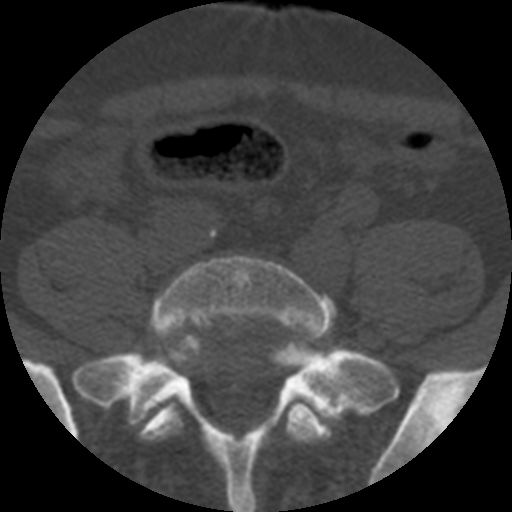
CT including the spine, one axial slice. Slice 52 of 508 in the series (ordered by position). Reconstruction kernel STANDARD. 120 kVp. Bone window (W 1800 / L 400 HU). 1.25 mm slice thickness. 512 × 512 image matrix, field of view 160 × 160 mm. Patient age 57 years. From the clinical record (not read from this slice): primary cancer: prostate.
Structures marked on this image (semi-automatic segmentation, software-assisted and operator-edited):
- L5 vertebra: bounding box [x1, y1, x2, y2] px = [138, 255, 335, 443]